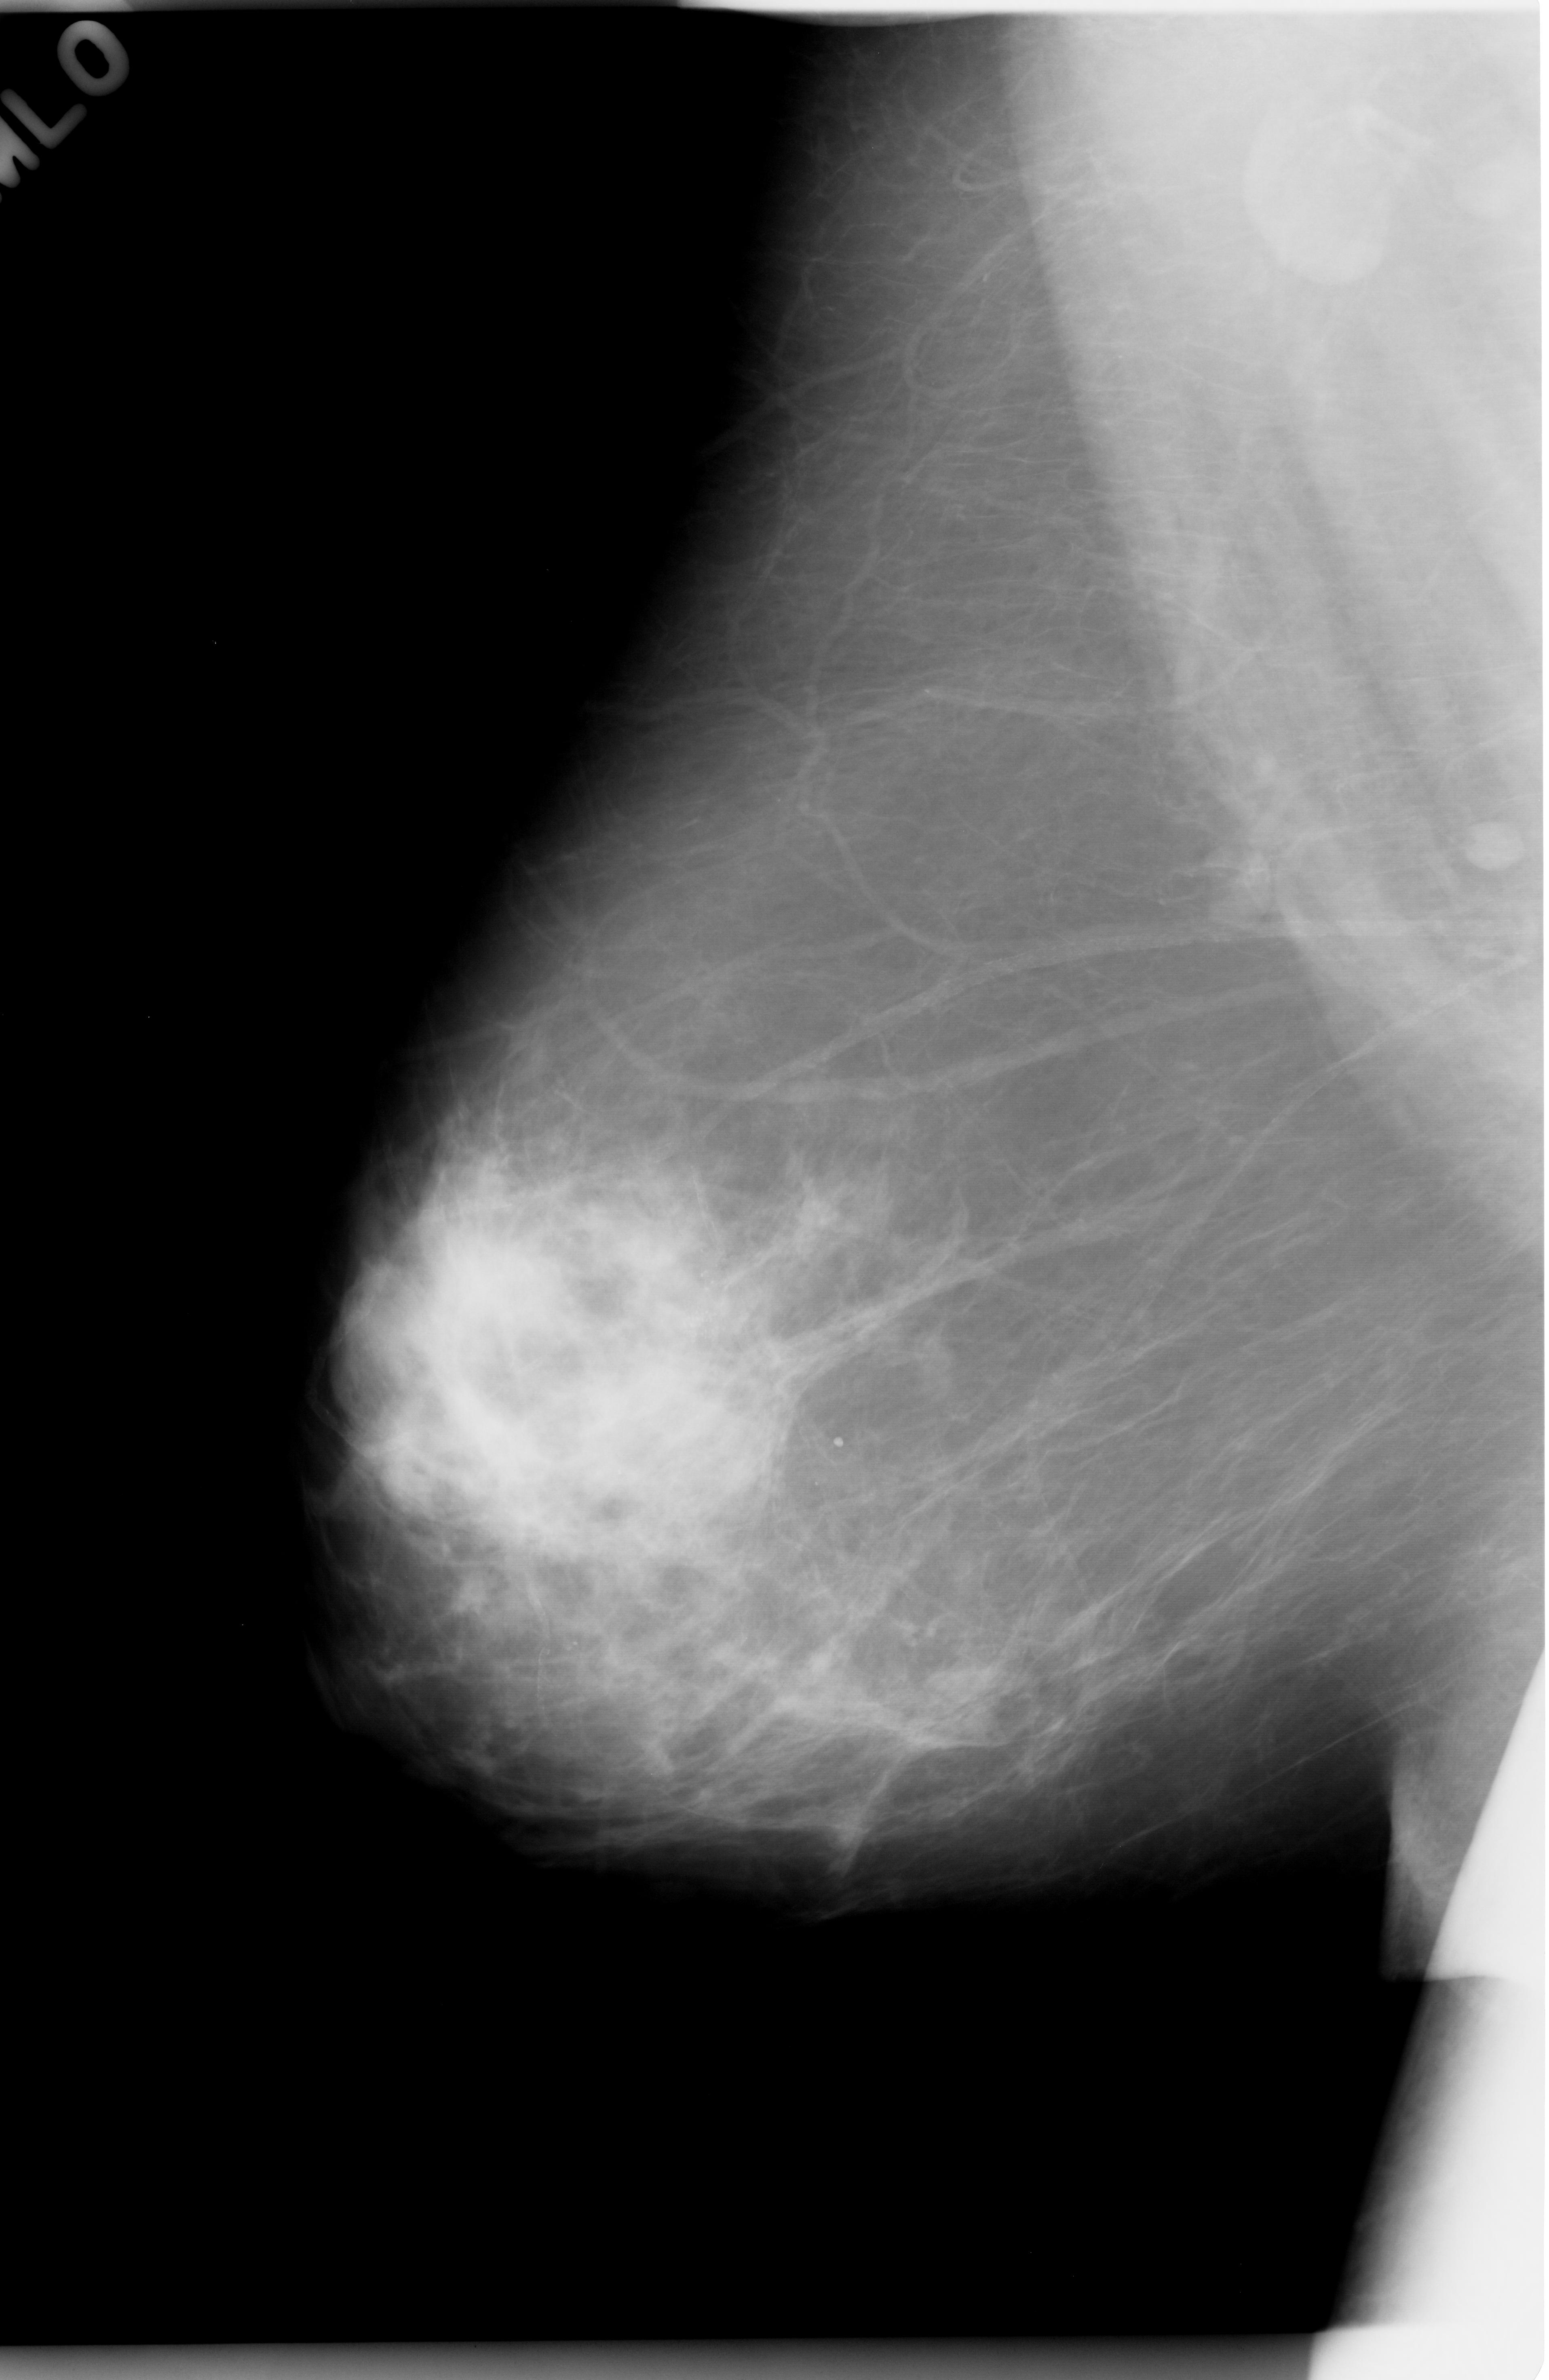
Mammogram (digitized film). Right breast. MLO view. Breast composition: scattered fibroglandular densities (BI-RADS density category 2 of 4). 1549 × 2380 image matrix.
Expert-marked regions of interest on this film, with their recorded descriptors:
- calcifications, morphology pleomorphic, distribution clustered; BI-RADS assessment category 5; subtlety rating 4 on a 1 (subtle) to 5 (obvious) scale; pathology (as recorded): malignant: bounding box [x1, y1, x2, y2] px = [633, 1215, 813, 1404]